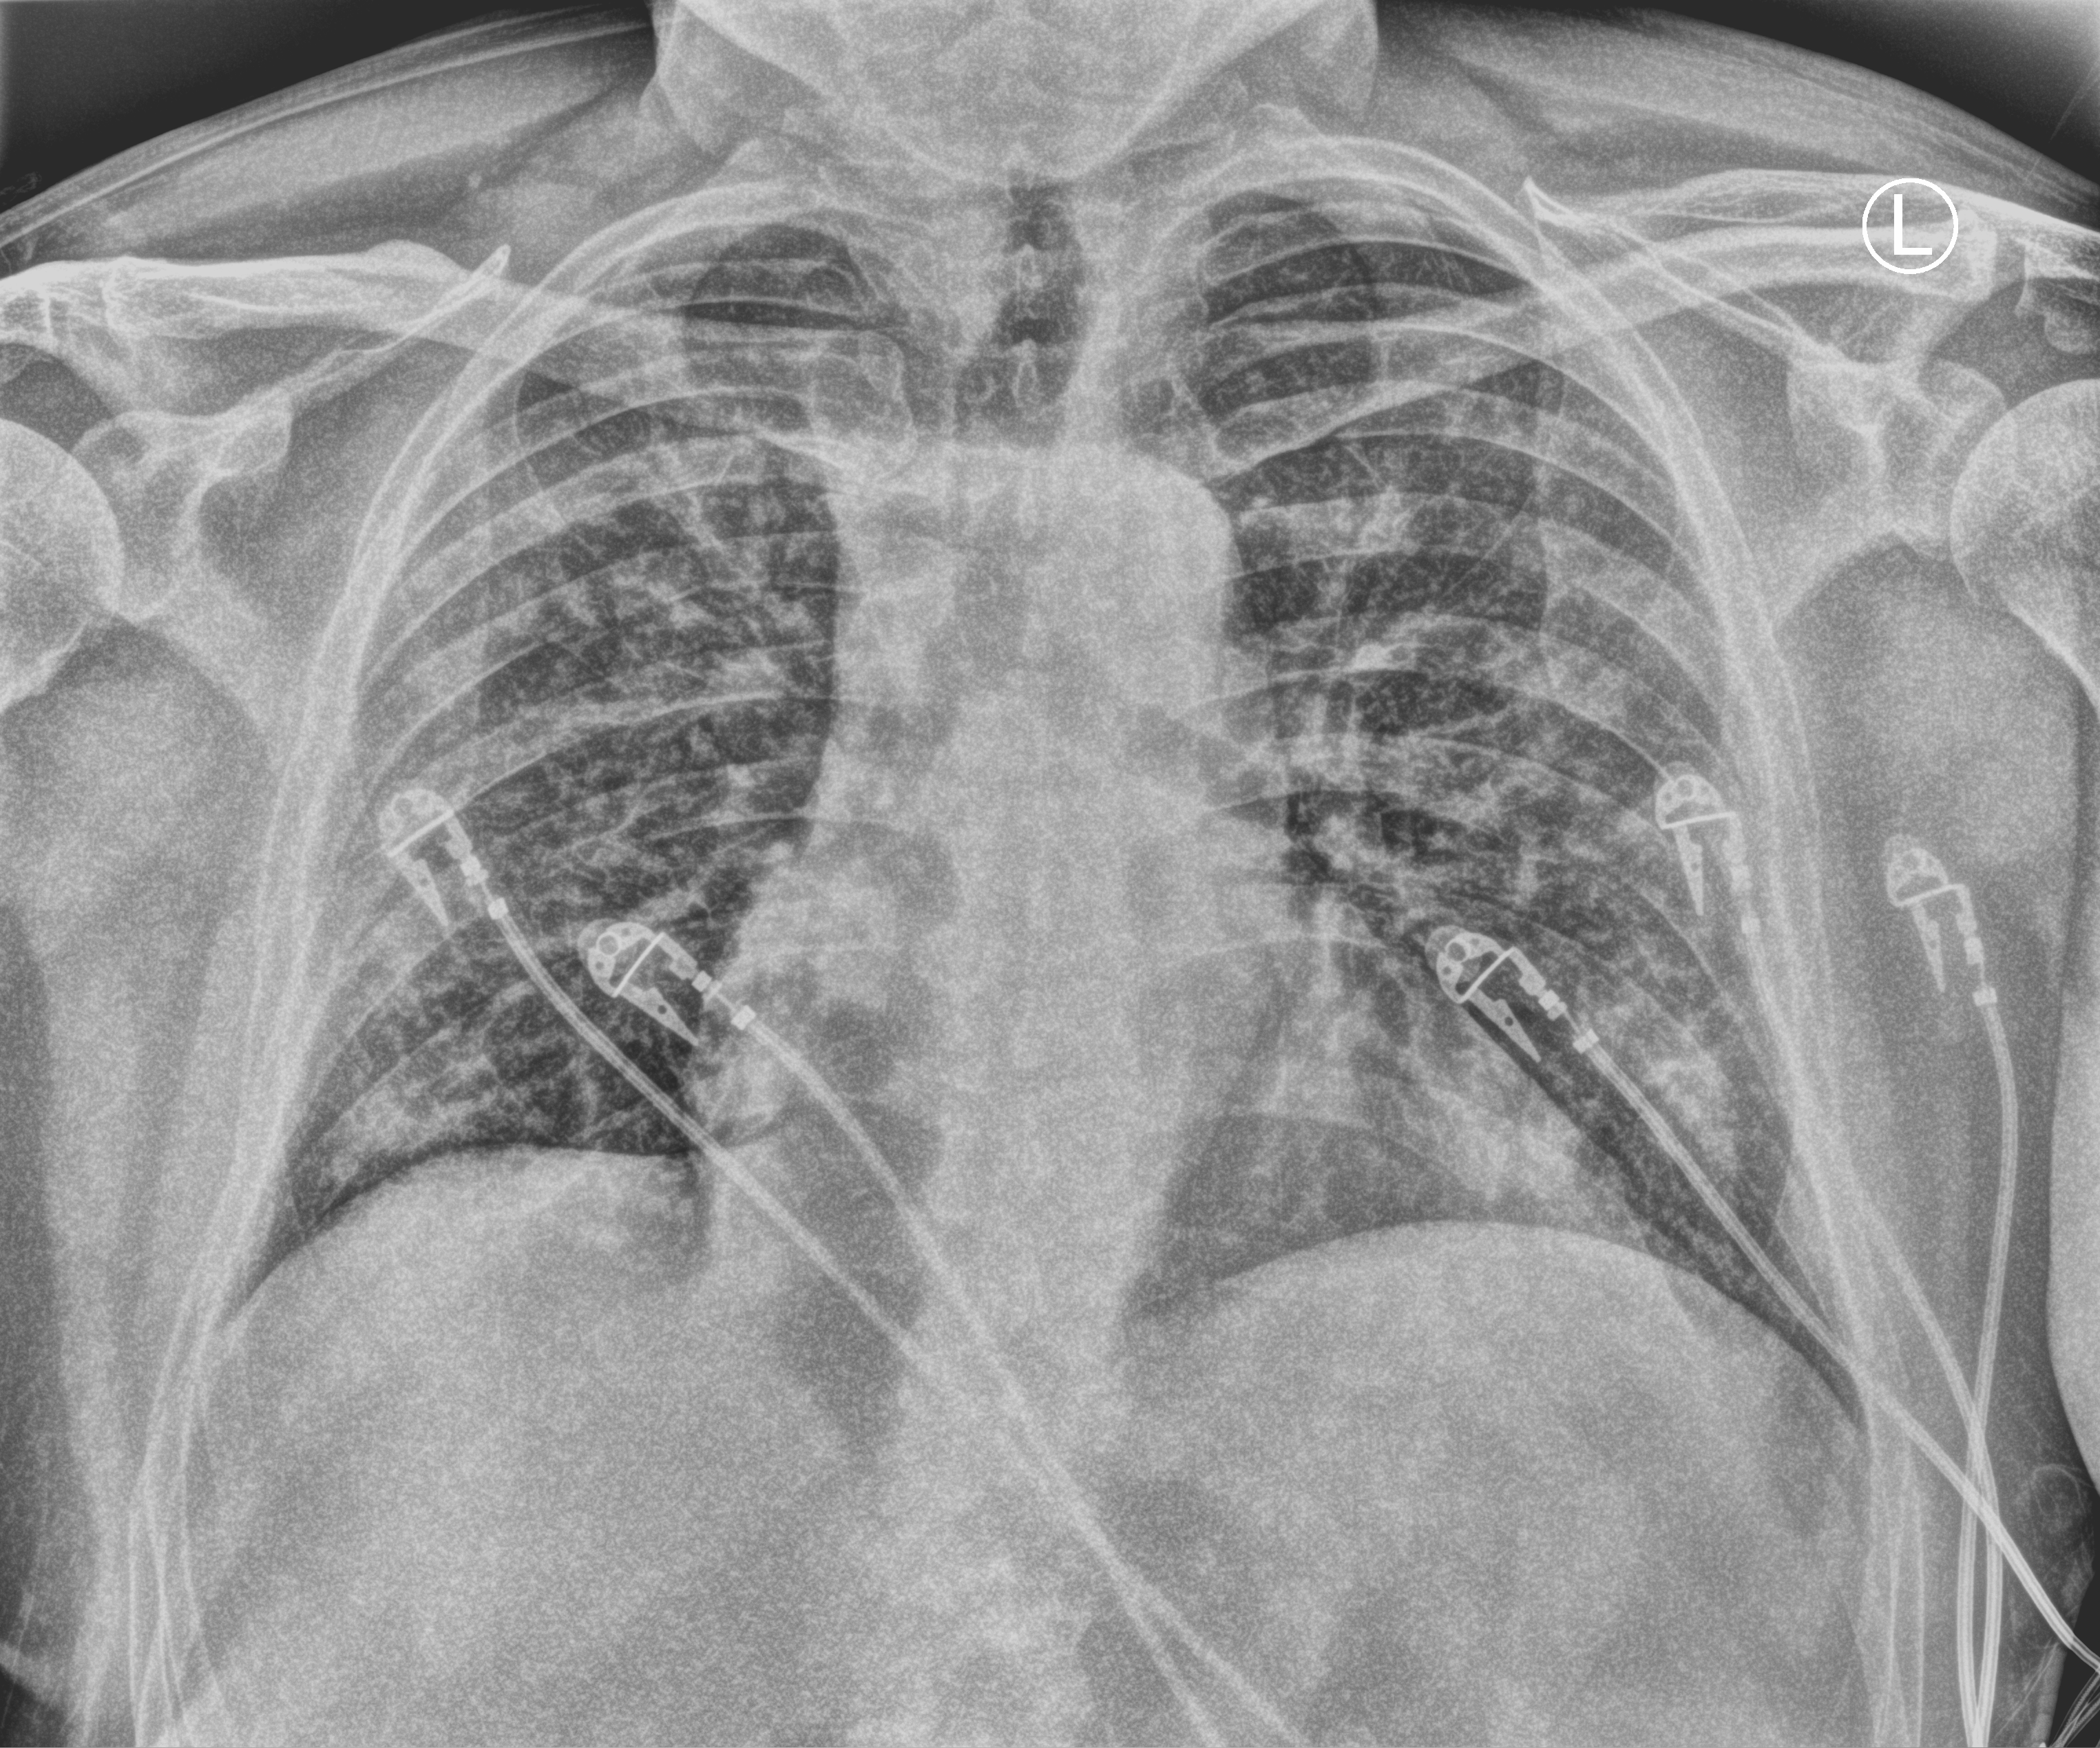
Chest X-ray (portable); anteroposterior (AP) projection. Male patient hospitalised with COVID-19, age 18–59 years.
Admission-level facts for this patient (not findings on this image; timing relative to this image not recorded):
- mechanically ventilated during this hospital stay: no
- hypertension (admission record): no
- admitted to intensive care during this hospital stay: no